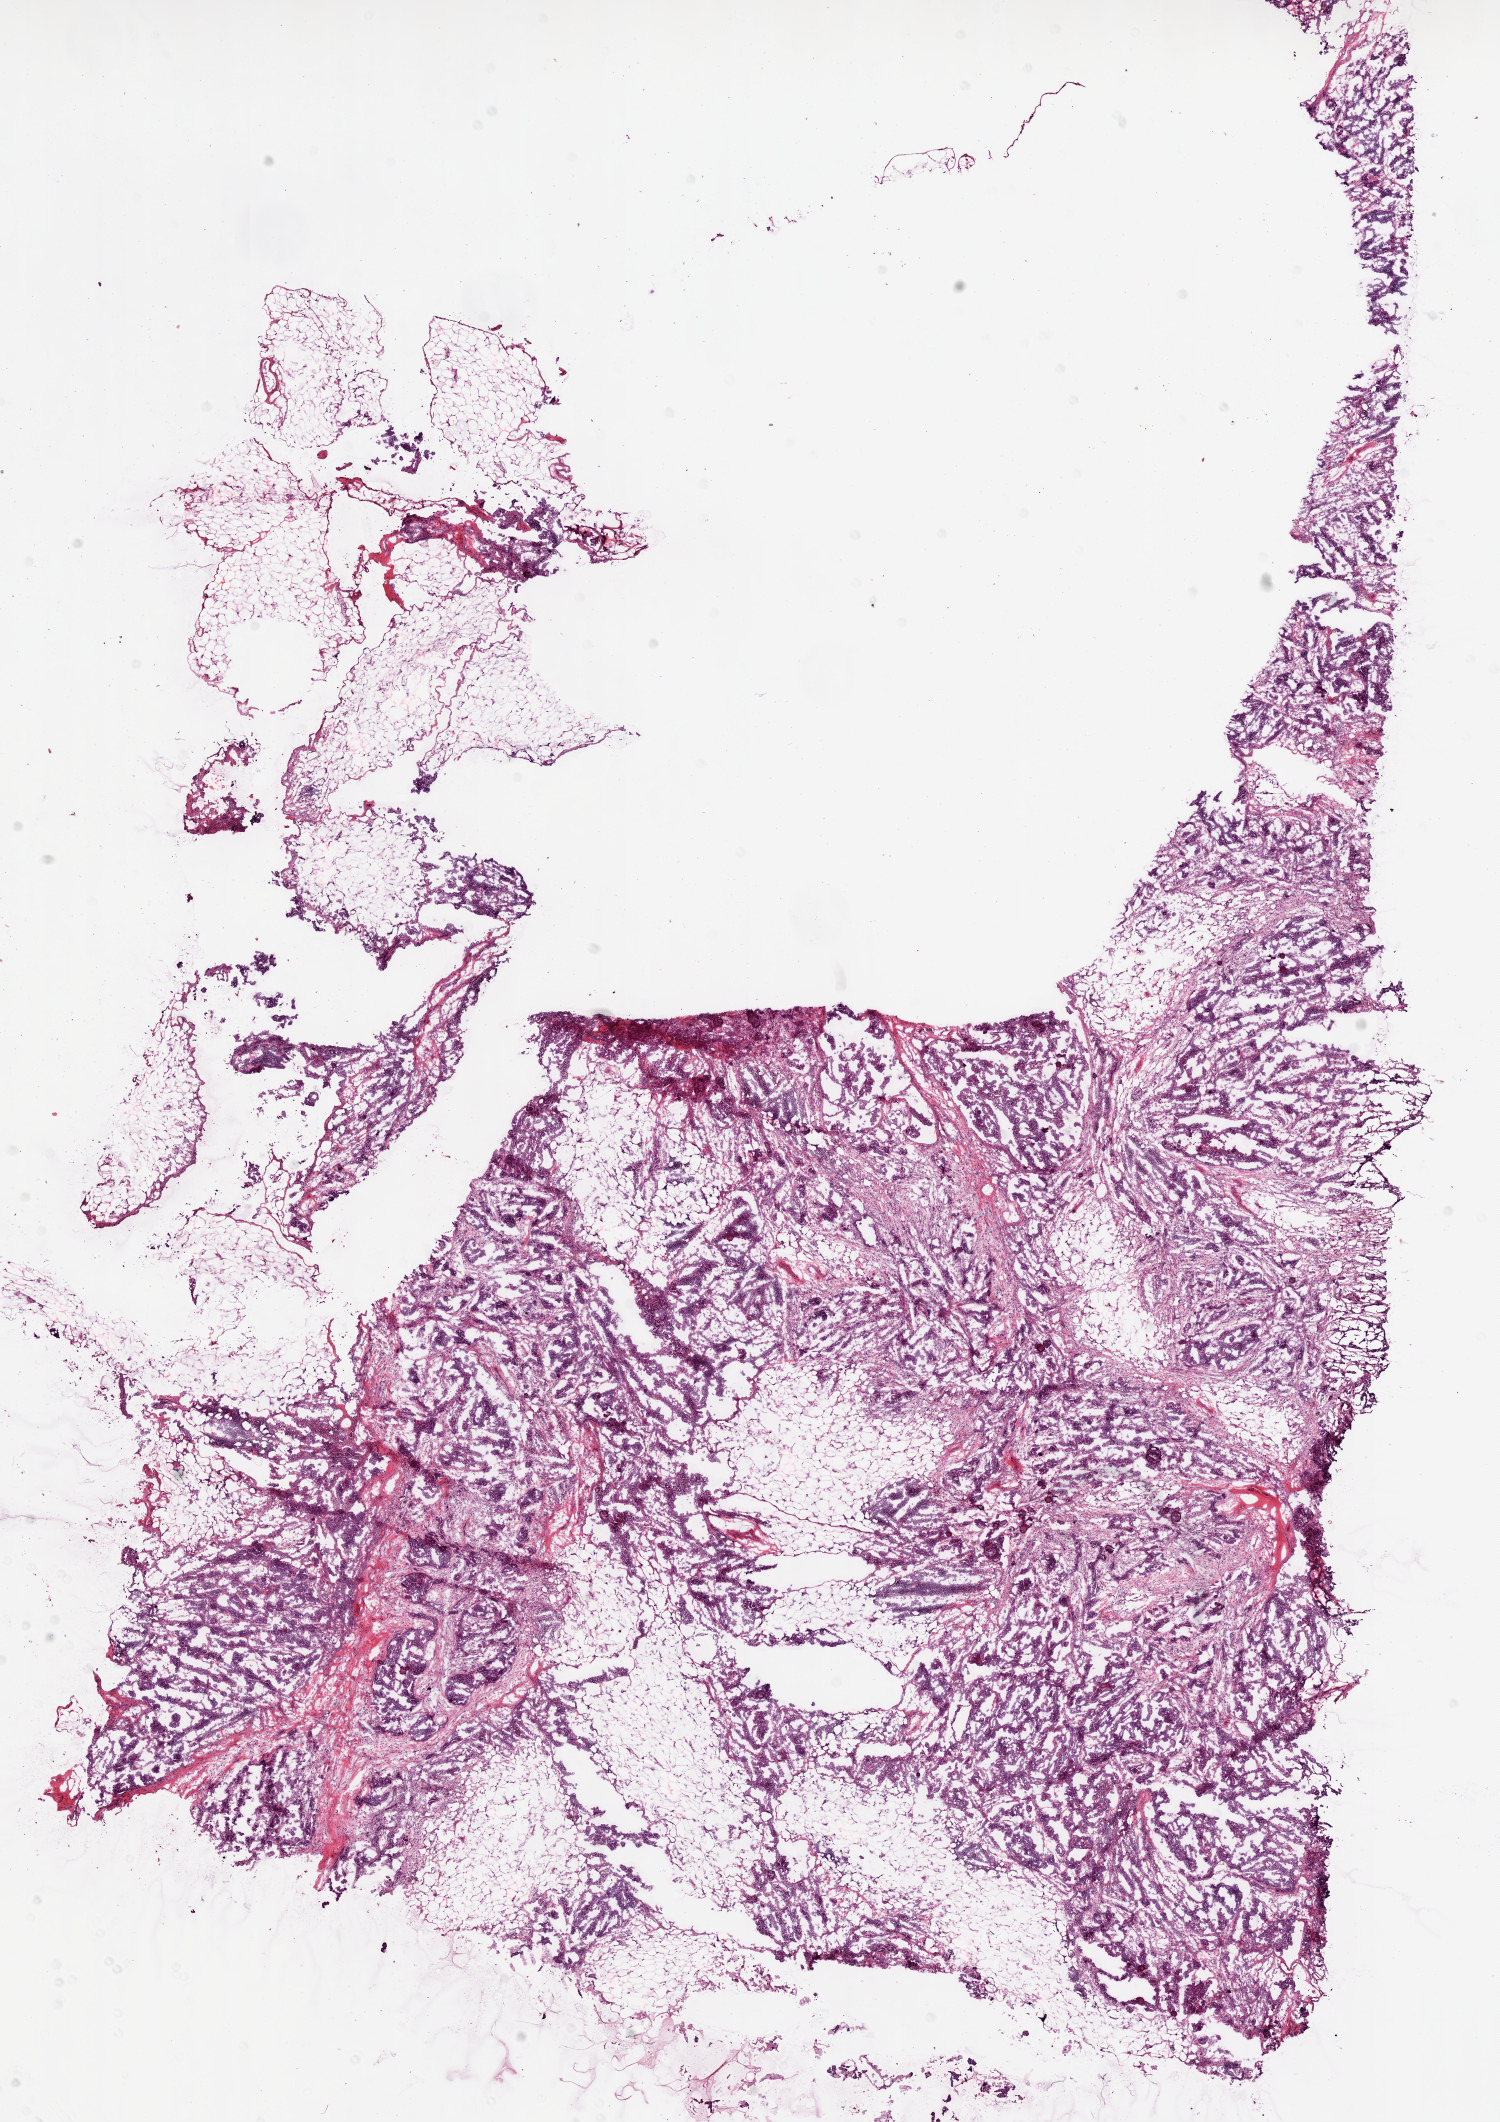
Digitized H&E tissue section (whole slide) — shown as a low-resolution overview of the whole scanned area (about 12.0 x 17.0 mm); frozen section from the bottom of the tissue portion; ovary, primary tumour sample. Patient: female, age at initial diagnosis 56 years. Histologic grade: G3 (poorly differentiated). Composition of this section per pathologist review: tumour cells 75%, tumour nuclei 80%, normal cells 0%, stromal cells 20%, necrosis 5%.
Histologic diagnosis: Serous cystadenocarcinoma, NOS. FIGO stage: IIIC.